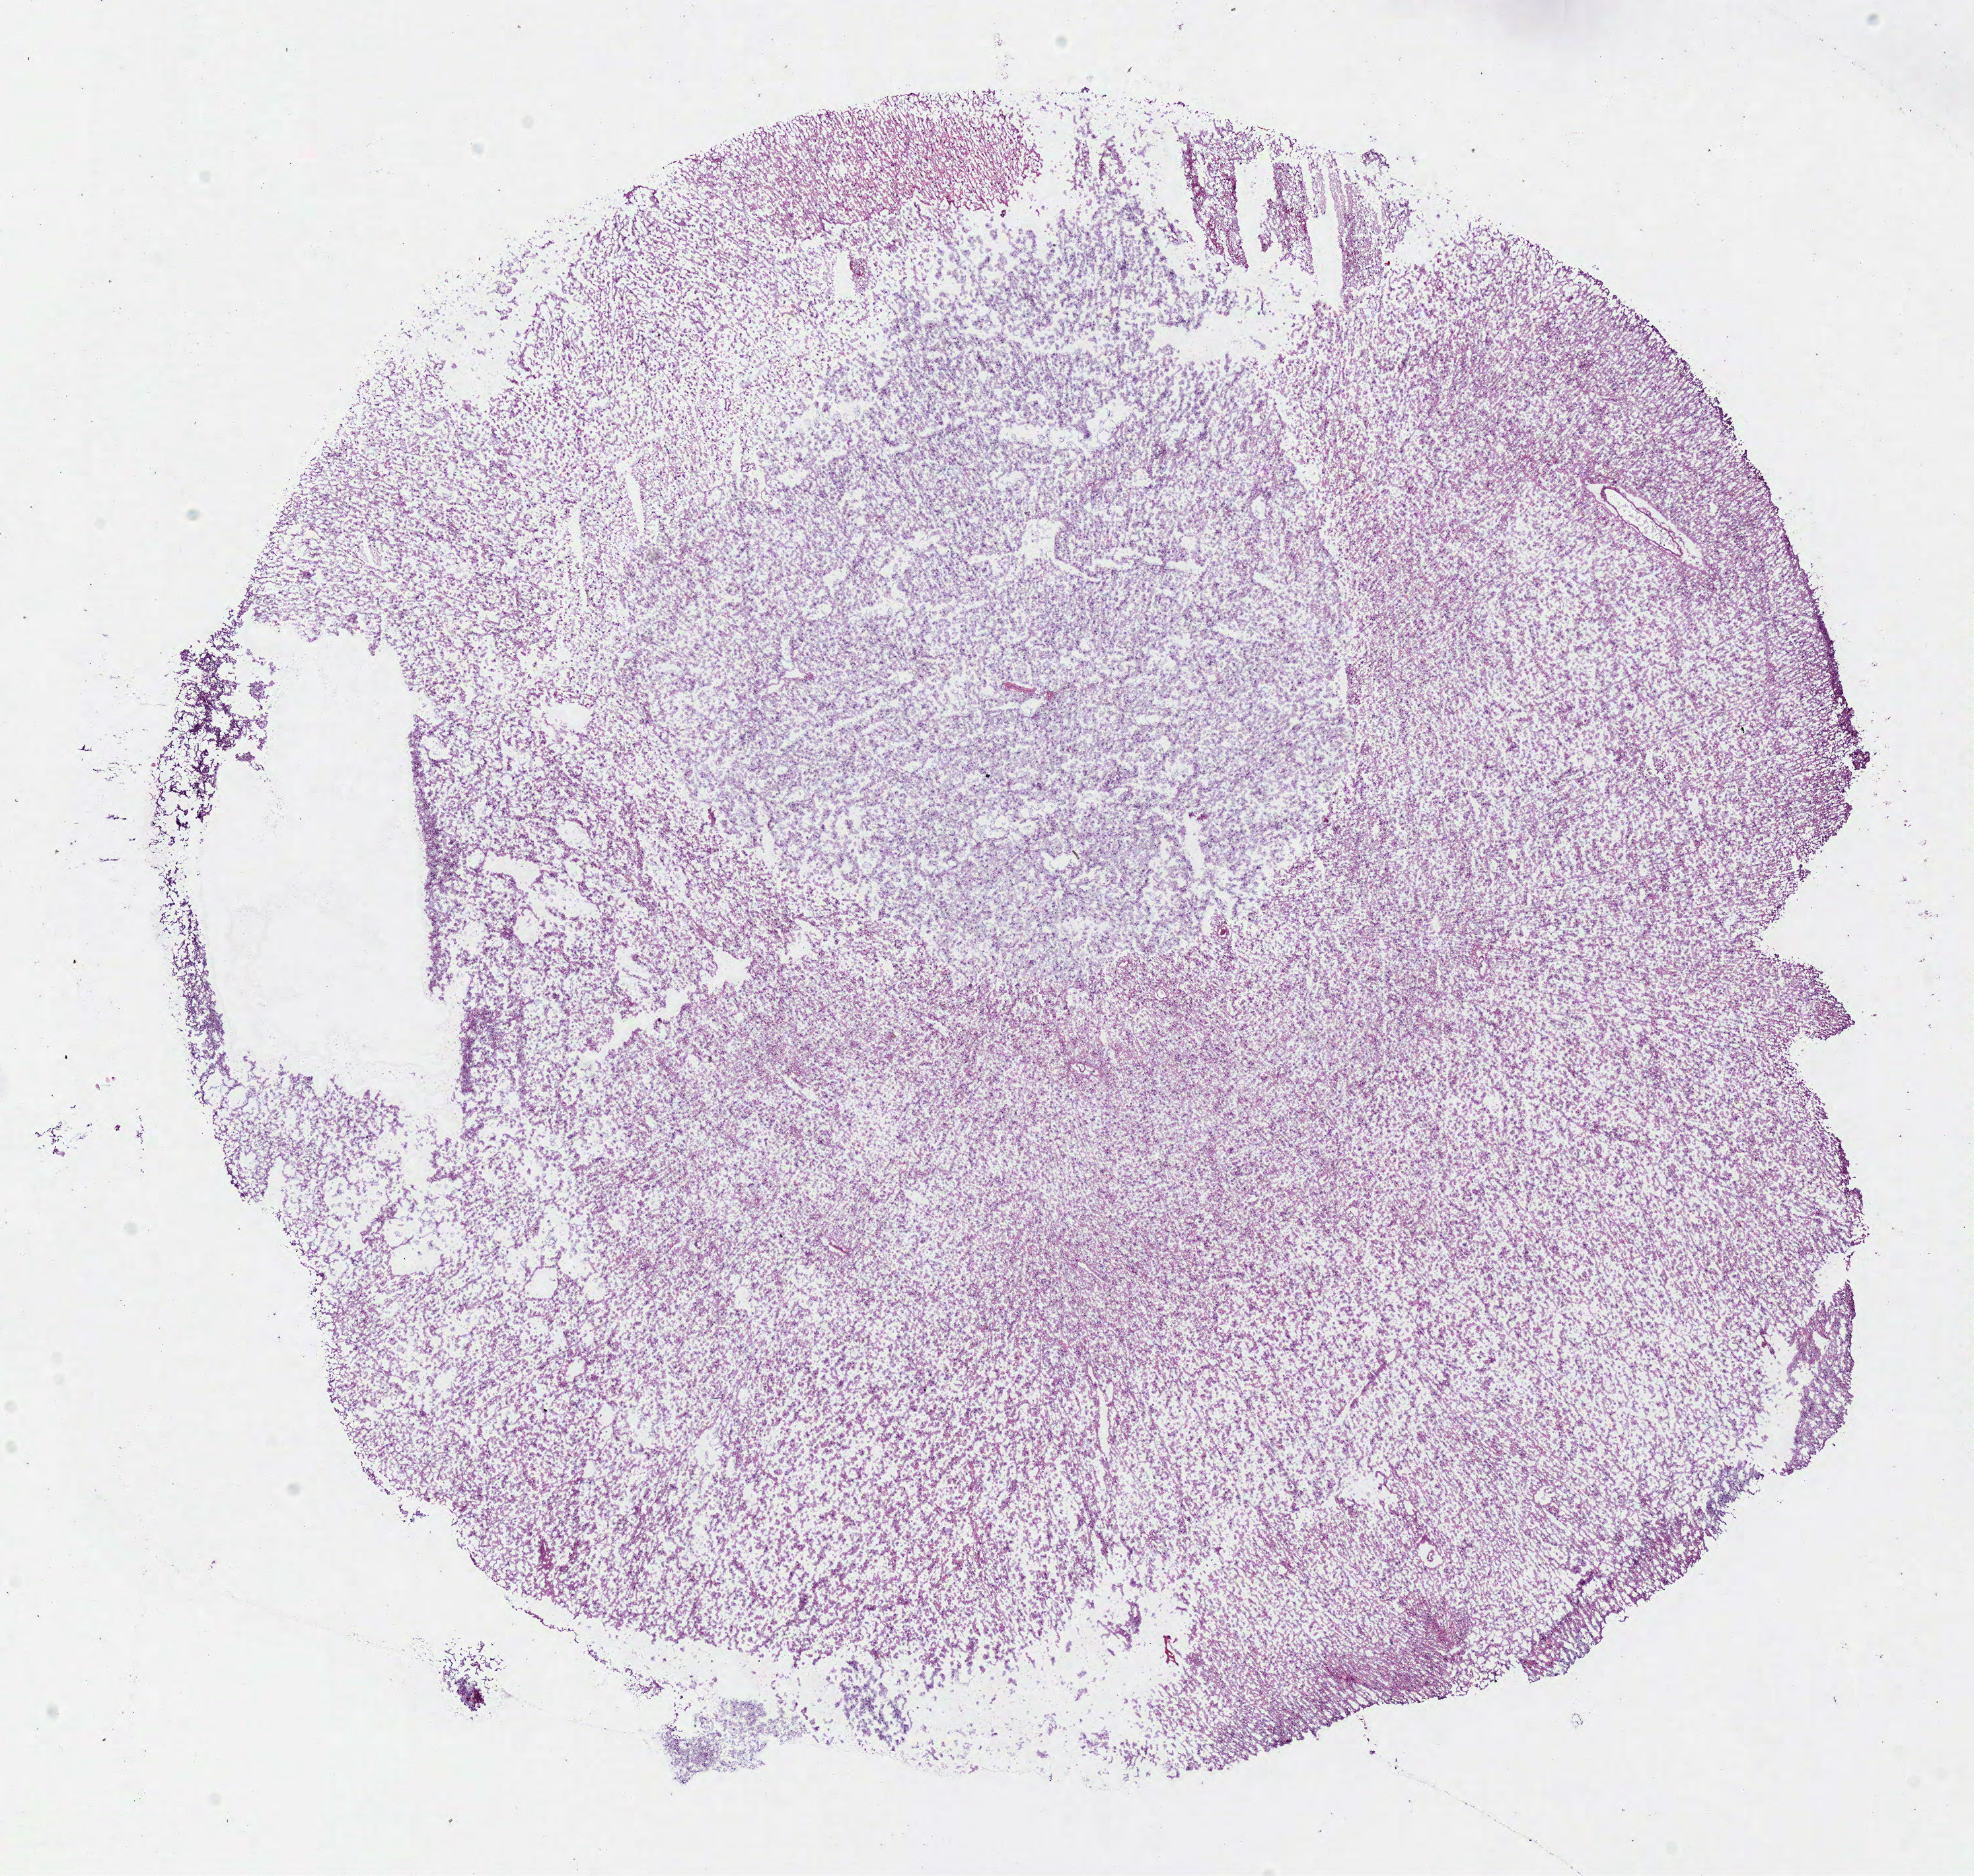
H&E-stained whole-slide image — low-resolution overview of the scanned area, about 11.7 x 11.2 mm (from a 40x scan), frozen section, sample: primary tumour, brain. Patient: male, age at initial diagnosis 31 years. Pathologist review of this section (percent, as recorded): tumour cells 100%, tumour nuclei 80%.
Histologic diagnosis: Mixed glioma (cerebrum).